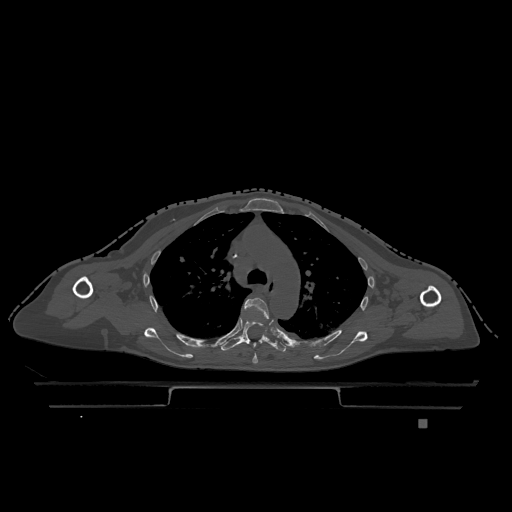
CT including the spine, one axial slice; slice 854 of 1317 in the series (ordered by position); bone window (W 1800 / L 400 HU); 0.5 mm slice thickness; 512 × 512 image matrix, field of view 500 × 500 mm. Patient: female, 74 years. From the clinical record (not read from this slice): primary cancer: lung; vertebrae with lytic lesions (as recorded): T1, T4, T5, T6, L4, L5.
Annotated regions visible in this slice (semi-automatically segmented with operator editing):
- T4 vertebra: bounding box [x1, y1, x2, y2] px = [244, 297, 269, 364]
- T5 vertebra: [221, 320, 288, 353]